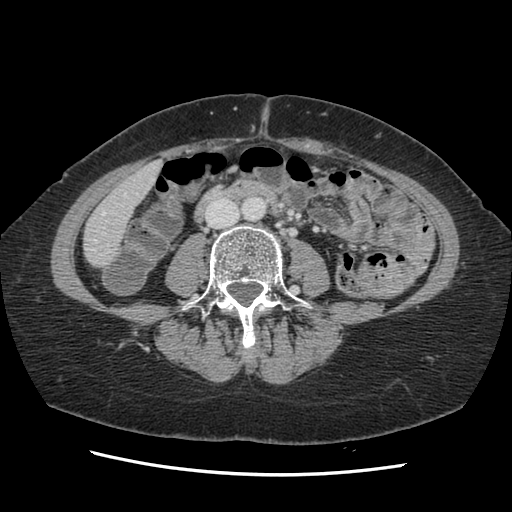
Contrast-enhanced abdominal CT, one axial slice. Slice 25 of 141 in the series (ordered by position). 120 kVp. Soft-tissue window (W 400 / L 40 HU). 2.5 mm slice thickness. 512 × 512 image matrix, field of view 330 × 330 mm. Female patient, age 61 years. From the clinical record (not read from this slice): diagnosis: colorectal cancer liver metastases, imaged before liver resection; multiple liver metastases: no; largest metastasis: 2.4 cm.
Annotated regions visible in this slice (outlined manually by an expert reader):
- hepatic veins: box from (x=93, y=175) to (x=139, y=251) px
- liver: (x=84, y=163)–(x=161, y=266)
- planned liver remnant (the part of the liver to remain after resection): (x=84, y=164)–(x=161, y=266)